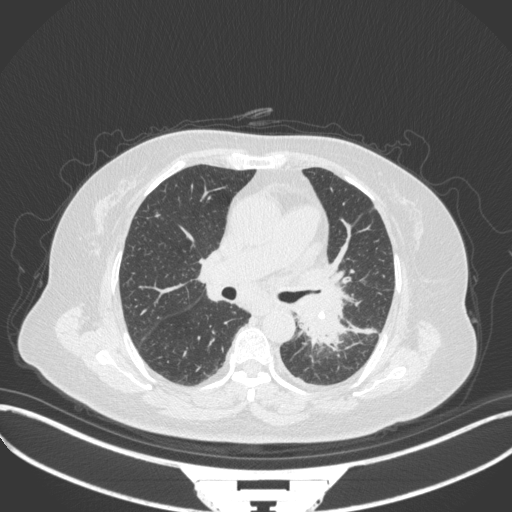
Chest CT, one axial slice. Position 200 of 328 along the scan axis. 120 kVp. Lung window (W 1500 / L -600 HU). 1 mm slice thickness. 512 × 512 image matrix, field of view 400 × 400 mm. Patient: female, 69 years. Case-level facts recorded for this patient, not image findings: clinical TNM (as recorded): T2b N3 M1.
Outlined on this slice (bounding box drawn by a radiologist):
- lung tumour (recorded histology: adenocarcinoma): bounding box (x1, y1, x2, y2) in pixels: (295, 294, 344, 351)